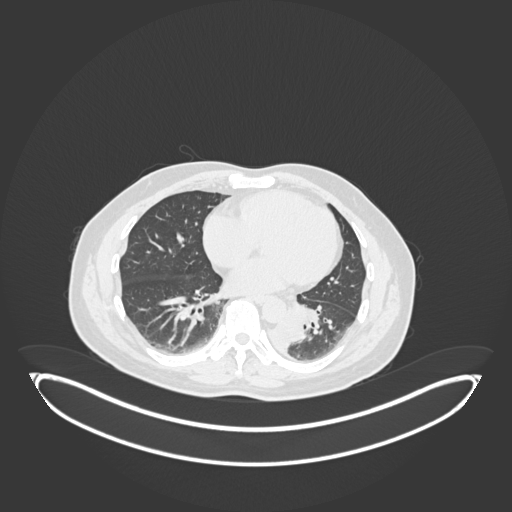
Chest CT, one axial slice; position 71 of 258 along the scan axis; reconstruction kernel B30f; lung window (W 1500 / L -600 HU); 1 mm slice thickness; 512 × 512 image matrix. Patient: male, 54 years. Case-level facts recorded for this patient, not image findings: clinical TNM (as recorded): T3 N0 M0.
Annotated regions visible in this slice (rectangle marked by the reading radiologist):
- lung tumour (recorded histology: squamous cell carcinoma): bounding box (x1, y1, x2, y2) in pixels: (266, 314, 310, 353)